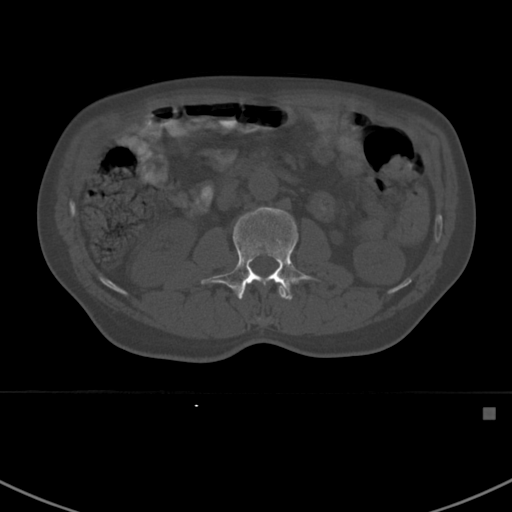
CT including the spine, one axial slice; slice 288 of 412 in the series (ordered by position); bone window (W 1800 / L 400 HU); 512 × 512 image matrix. Patient: male, 59 years. From the clinical record (not read from this slice): primary cancer: prostate.
Annotated regions visible in this slice (semi-automatic segmentation, software-assisted and operator-edited):
- L1 vertebra: bounding box [x1, y1, x2, y2] px = [257, 287, 287, 322]
- L2 vertebra: [201, 207, 318, 300]